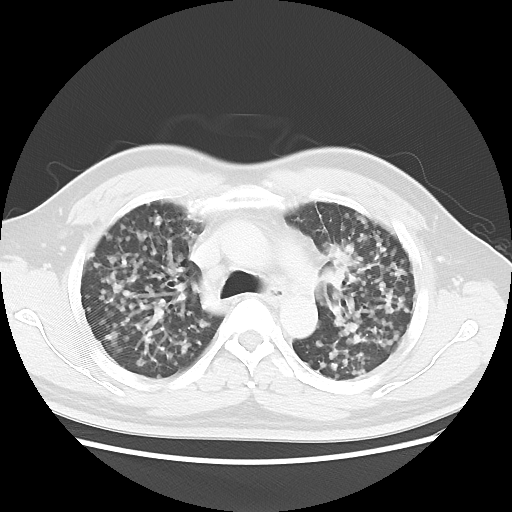
Chest CT, one axial slice. Position 27 of 40 along the scan axis. Reconstruction kernel LUNG. Lung window (W 1500 / L -600 HU). 5 mm slice thickness. 512 × 512 image matrix. Male patient, age 41 years. From the clinical record (not read from this slice): clinical TNM (as recorded): T1c N3 M1b.
Outlined on this slice (bounding box drawn by a radiologist):
- lung tumour (recorded histology: adenocarcinoma): bounding box [x1, y1, x2, y2] px = [326, 236, 362, 300]